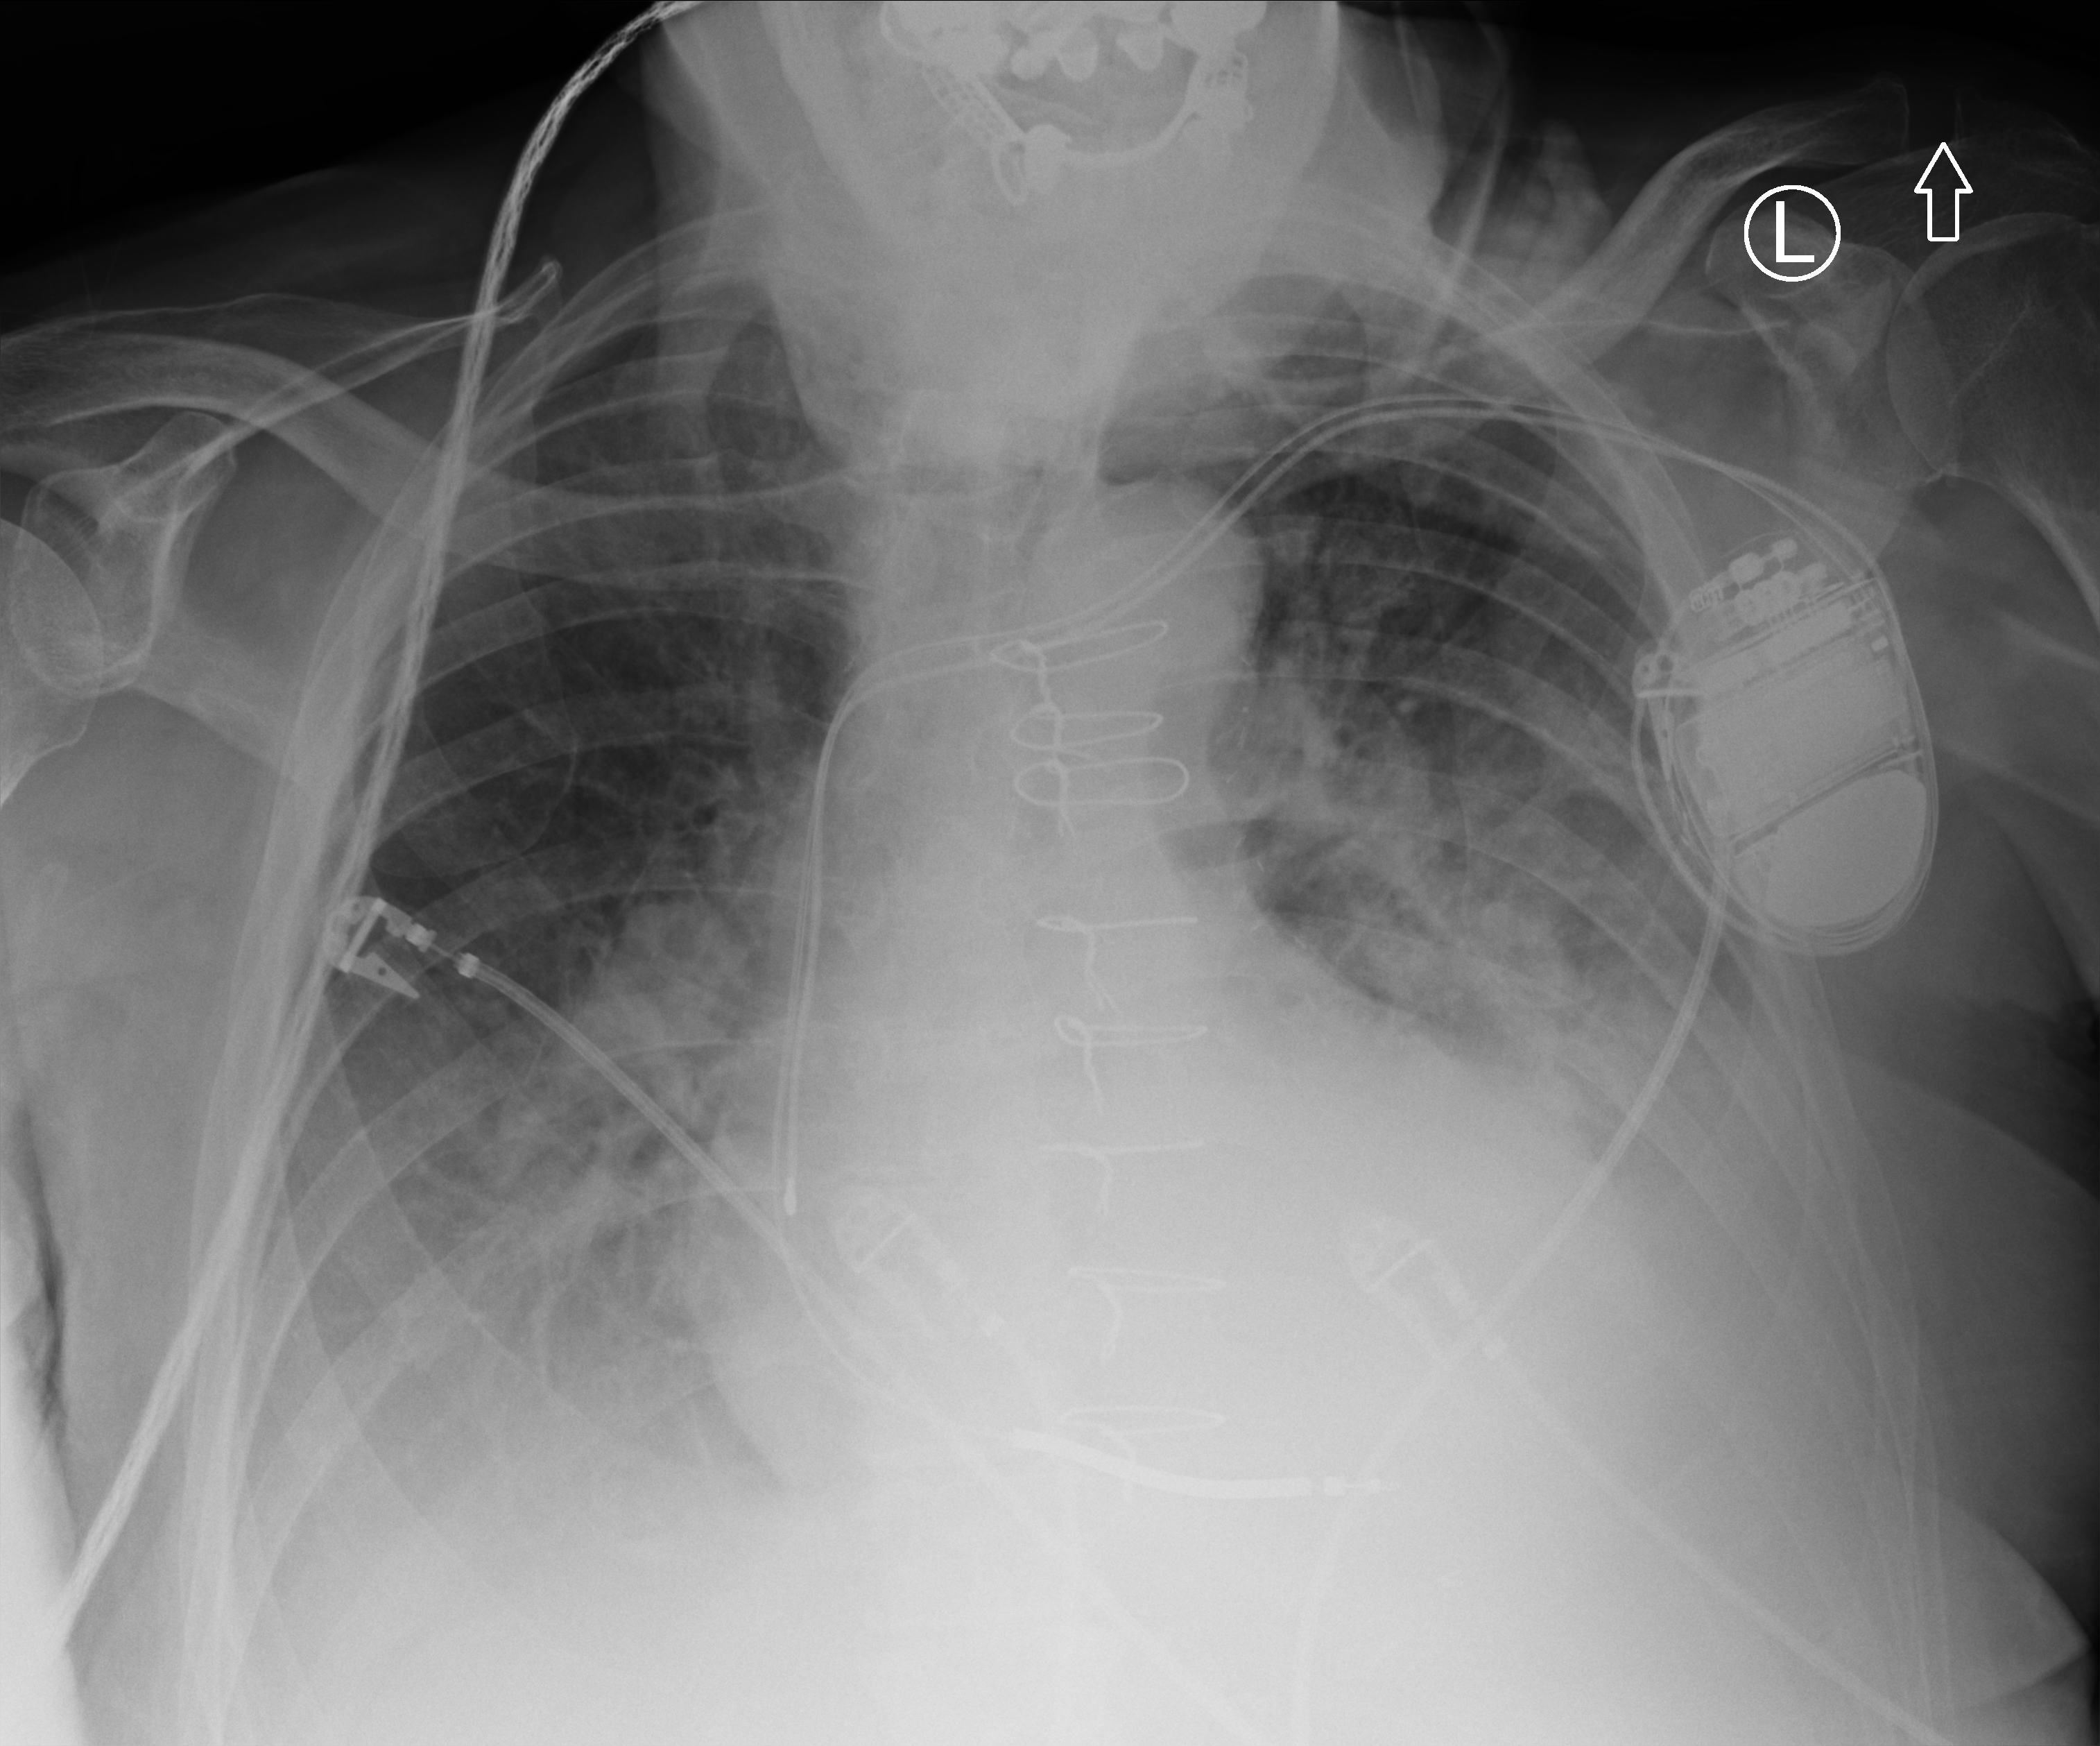
Portable chest radiograph. Patient hospitalised with COVID-19; male, aged 75–90 years.
From the hospital-stay record, not from the radiograph (when in the stay this image was taken is not recorded): mechanically ventilated during this hospital stay: yes; length of hospital stay: 11 days; admitted to intensive care during this hospital stay: yes.